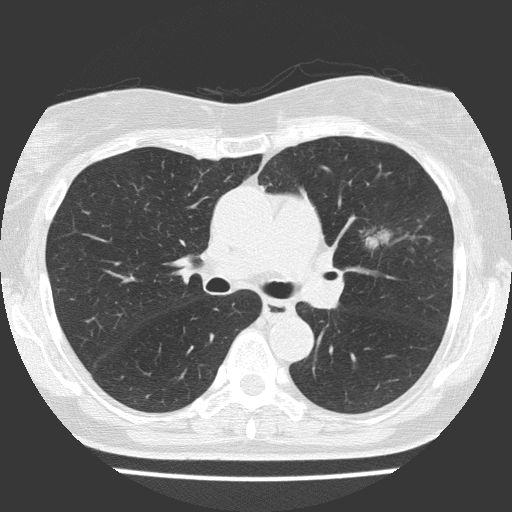
Low-dose screening chest CT, one axial slice; position 91 of 151 along the scan axis; reconstruction kernel FC51; lung window (W 1500 / L -600 HU); 2 mm slice thickness; 512 × 512 image matrix, field of view 309 × 309 mm.
Structures marked on this image (outlined manually by an expert reader):
- lesion 1 (tumor, upper lobe of left lung): bounding box [x1, y1, x2, y2] px = [366, 231, 390, 249]